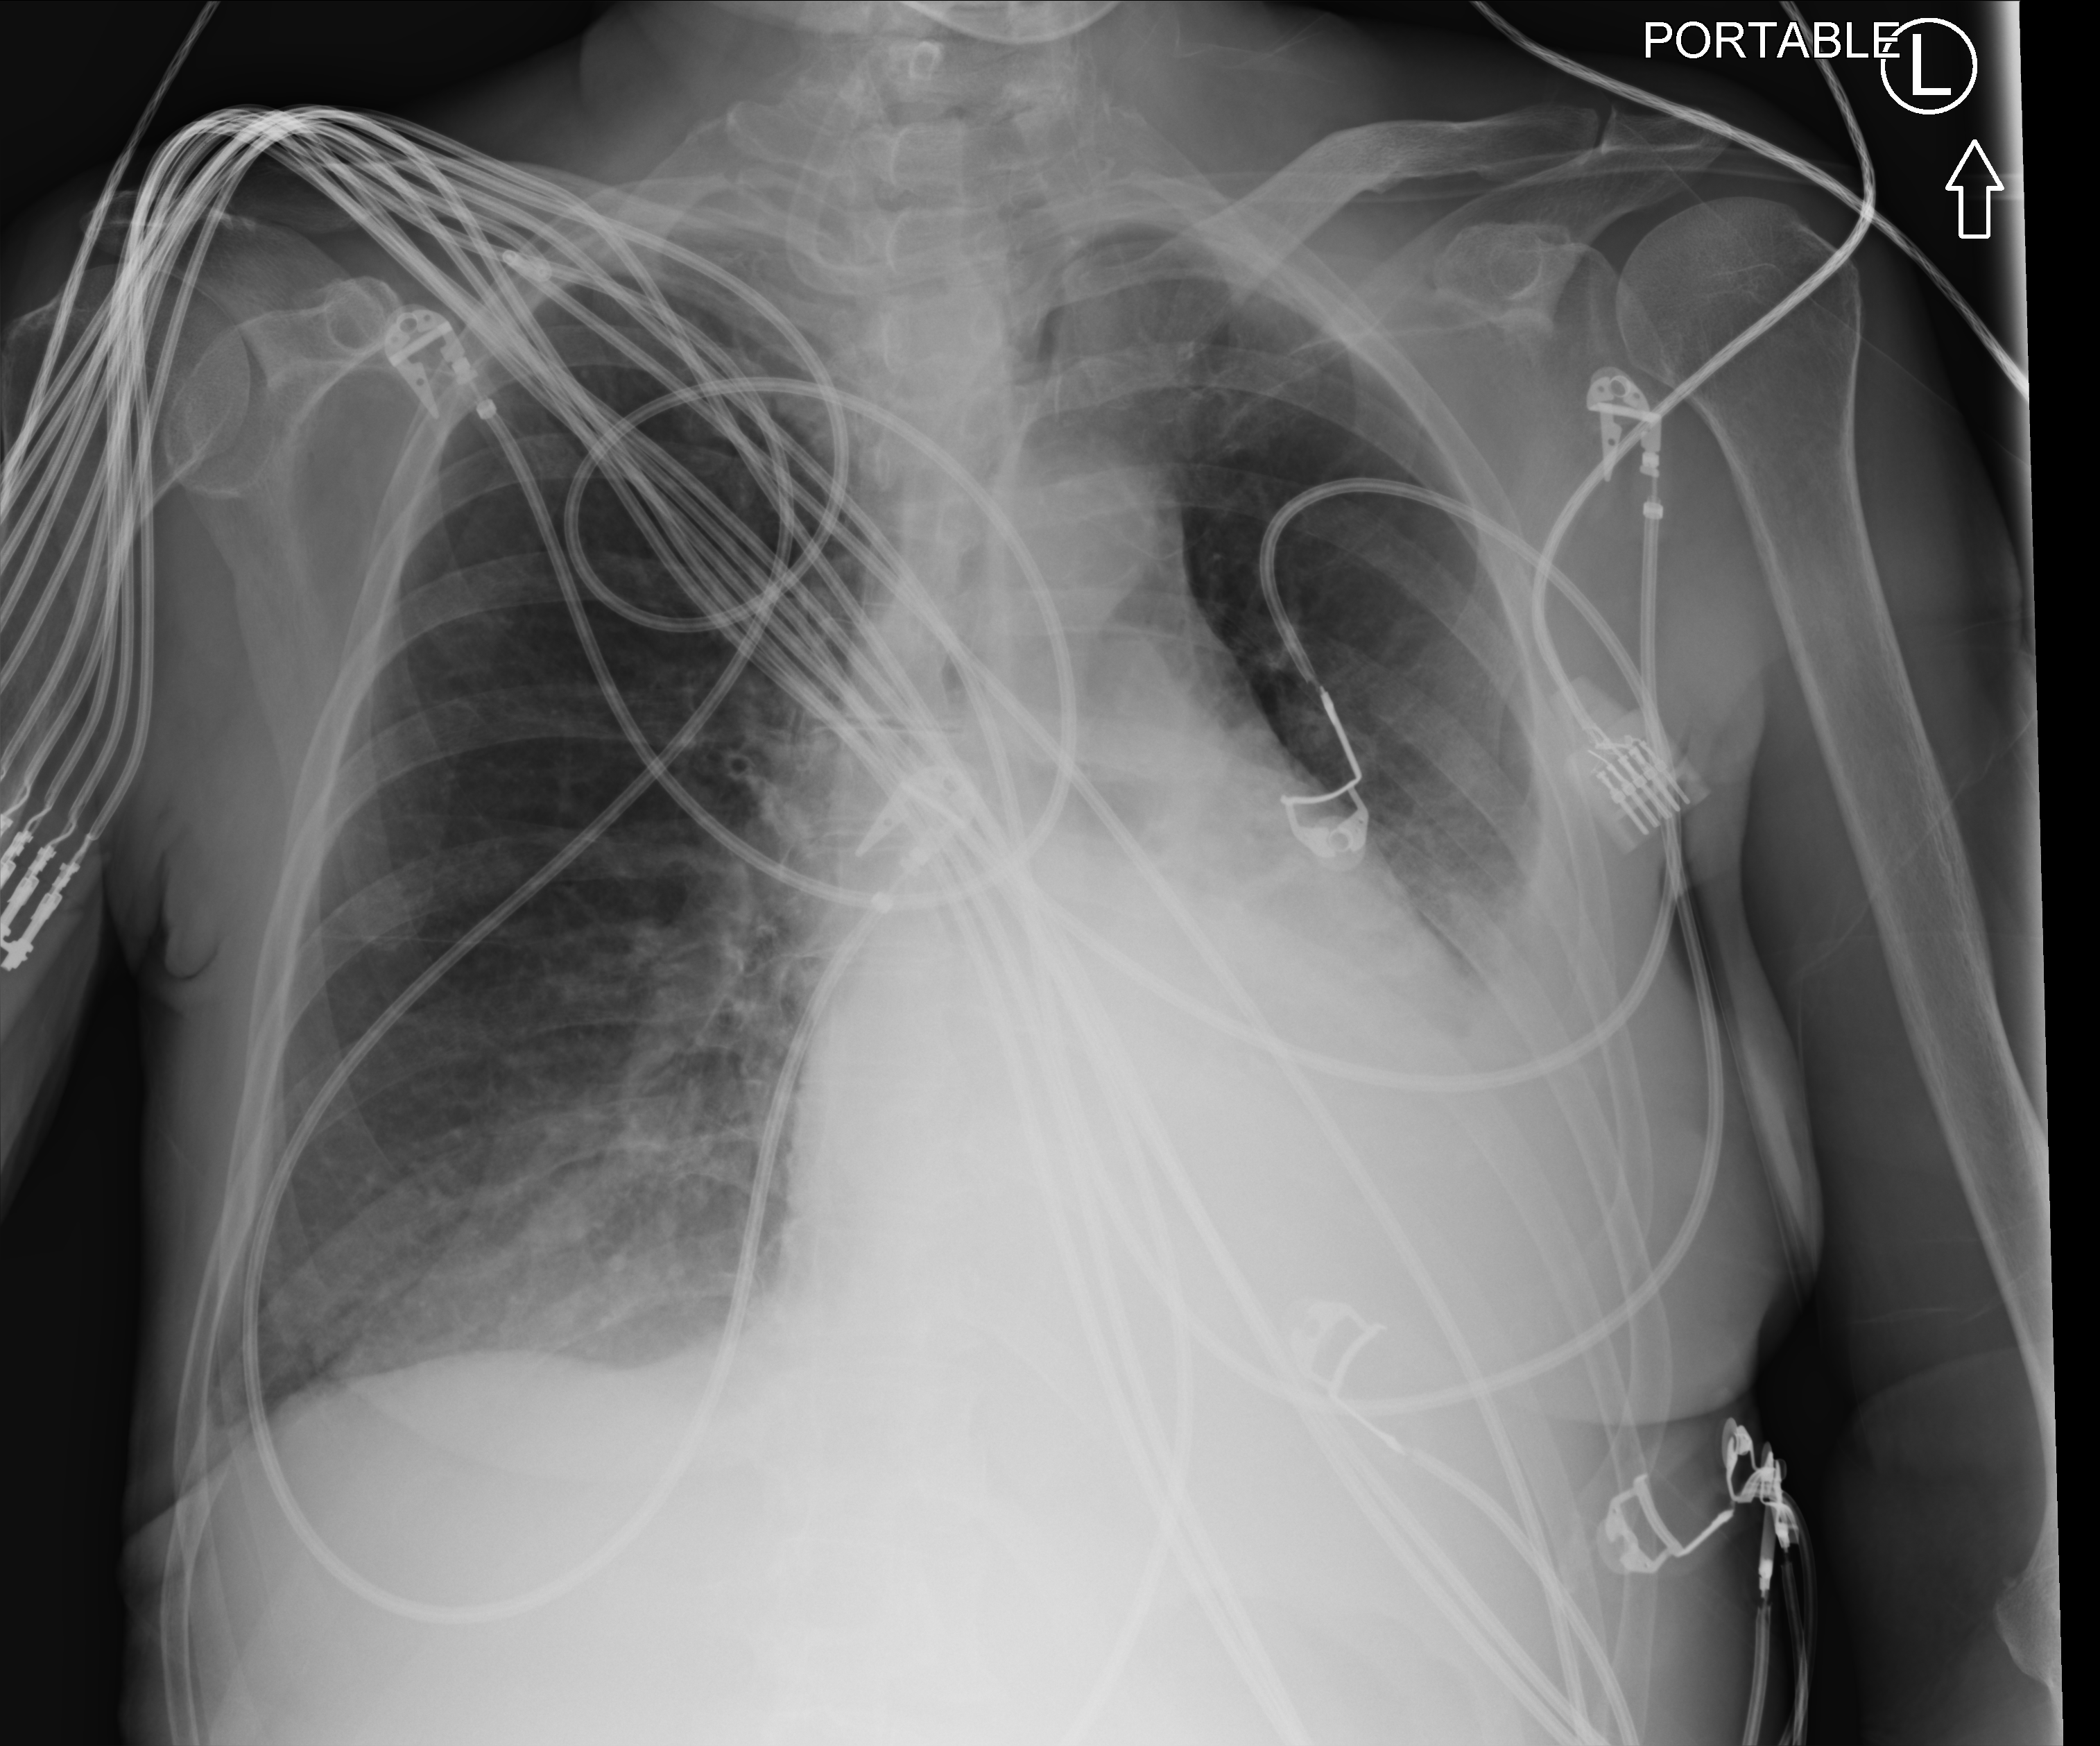
Chest X-ray (portable), anteroposterior (AP) projection. Female patient hospitalised with COVID-19, age 60–74 years.
Admission-level facts for this patient (not findings on this image; timing relative to this image not recorded):
- admitted to intensive care during this hospital stay: yes
- length of hospital stay: 38 days